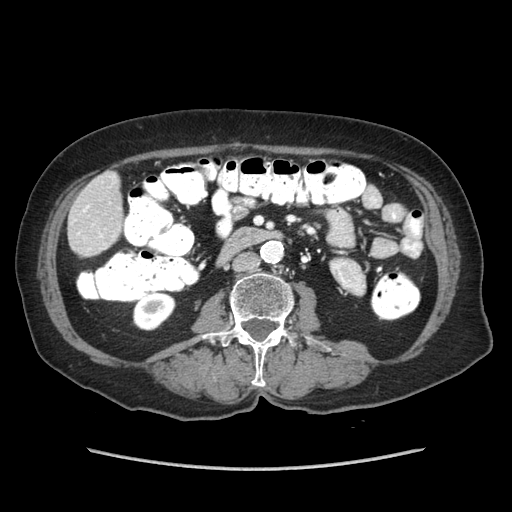
Contrast-enhanced abdominal CT (liver protocol), one axial slice; slice 11 of 89 in the series (ordered by position); reconstruction kernel STANDARD; 140 kVp; soft-tissue window (W 400 / L 40 HU); 2.5 mm slice thickness; 512 × 512 image matrix, field of view 360 × 360 mm. Case-level facts recorded for this patient, not image findings: diagnosis: hepatocellular carcinoma (patient treated with transarterial chemoembolisation; whether this scan precedes or follows treatment is not stated here); TNM stage (as recorded): Stage-IIIA; Child-Pugh class: A; tumour size: 11 cm.
Structures marked on this image (semi-automatic segmentation, software-assisted and operator-edited):
- liver parenchyma outside the tumour (the mass and vessels are separate outlines, so this box may not span the whole liver): bounding box (x1, y1, x2, y2) in pixels: (68, 172, 122, 256)
- liver vessels: (87, 206, 89, 208)